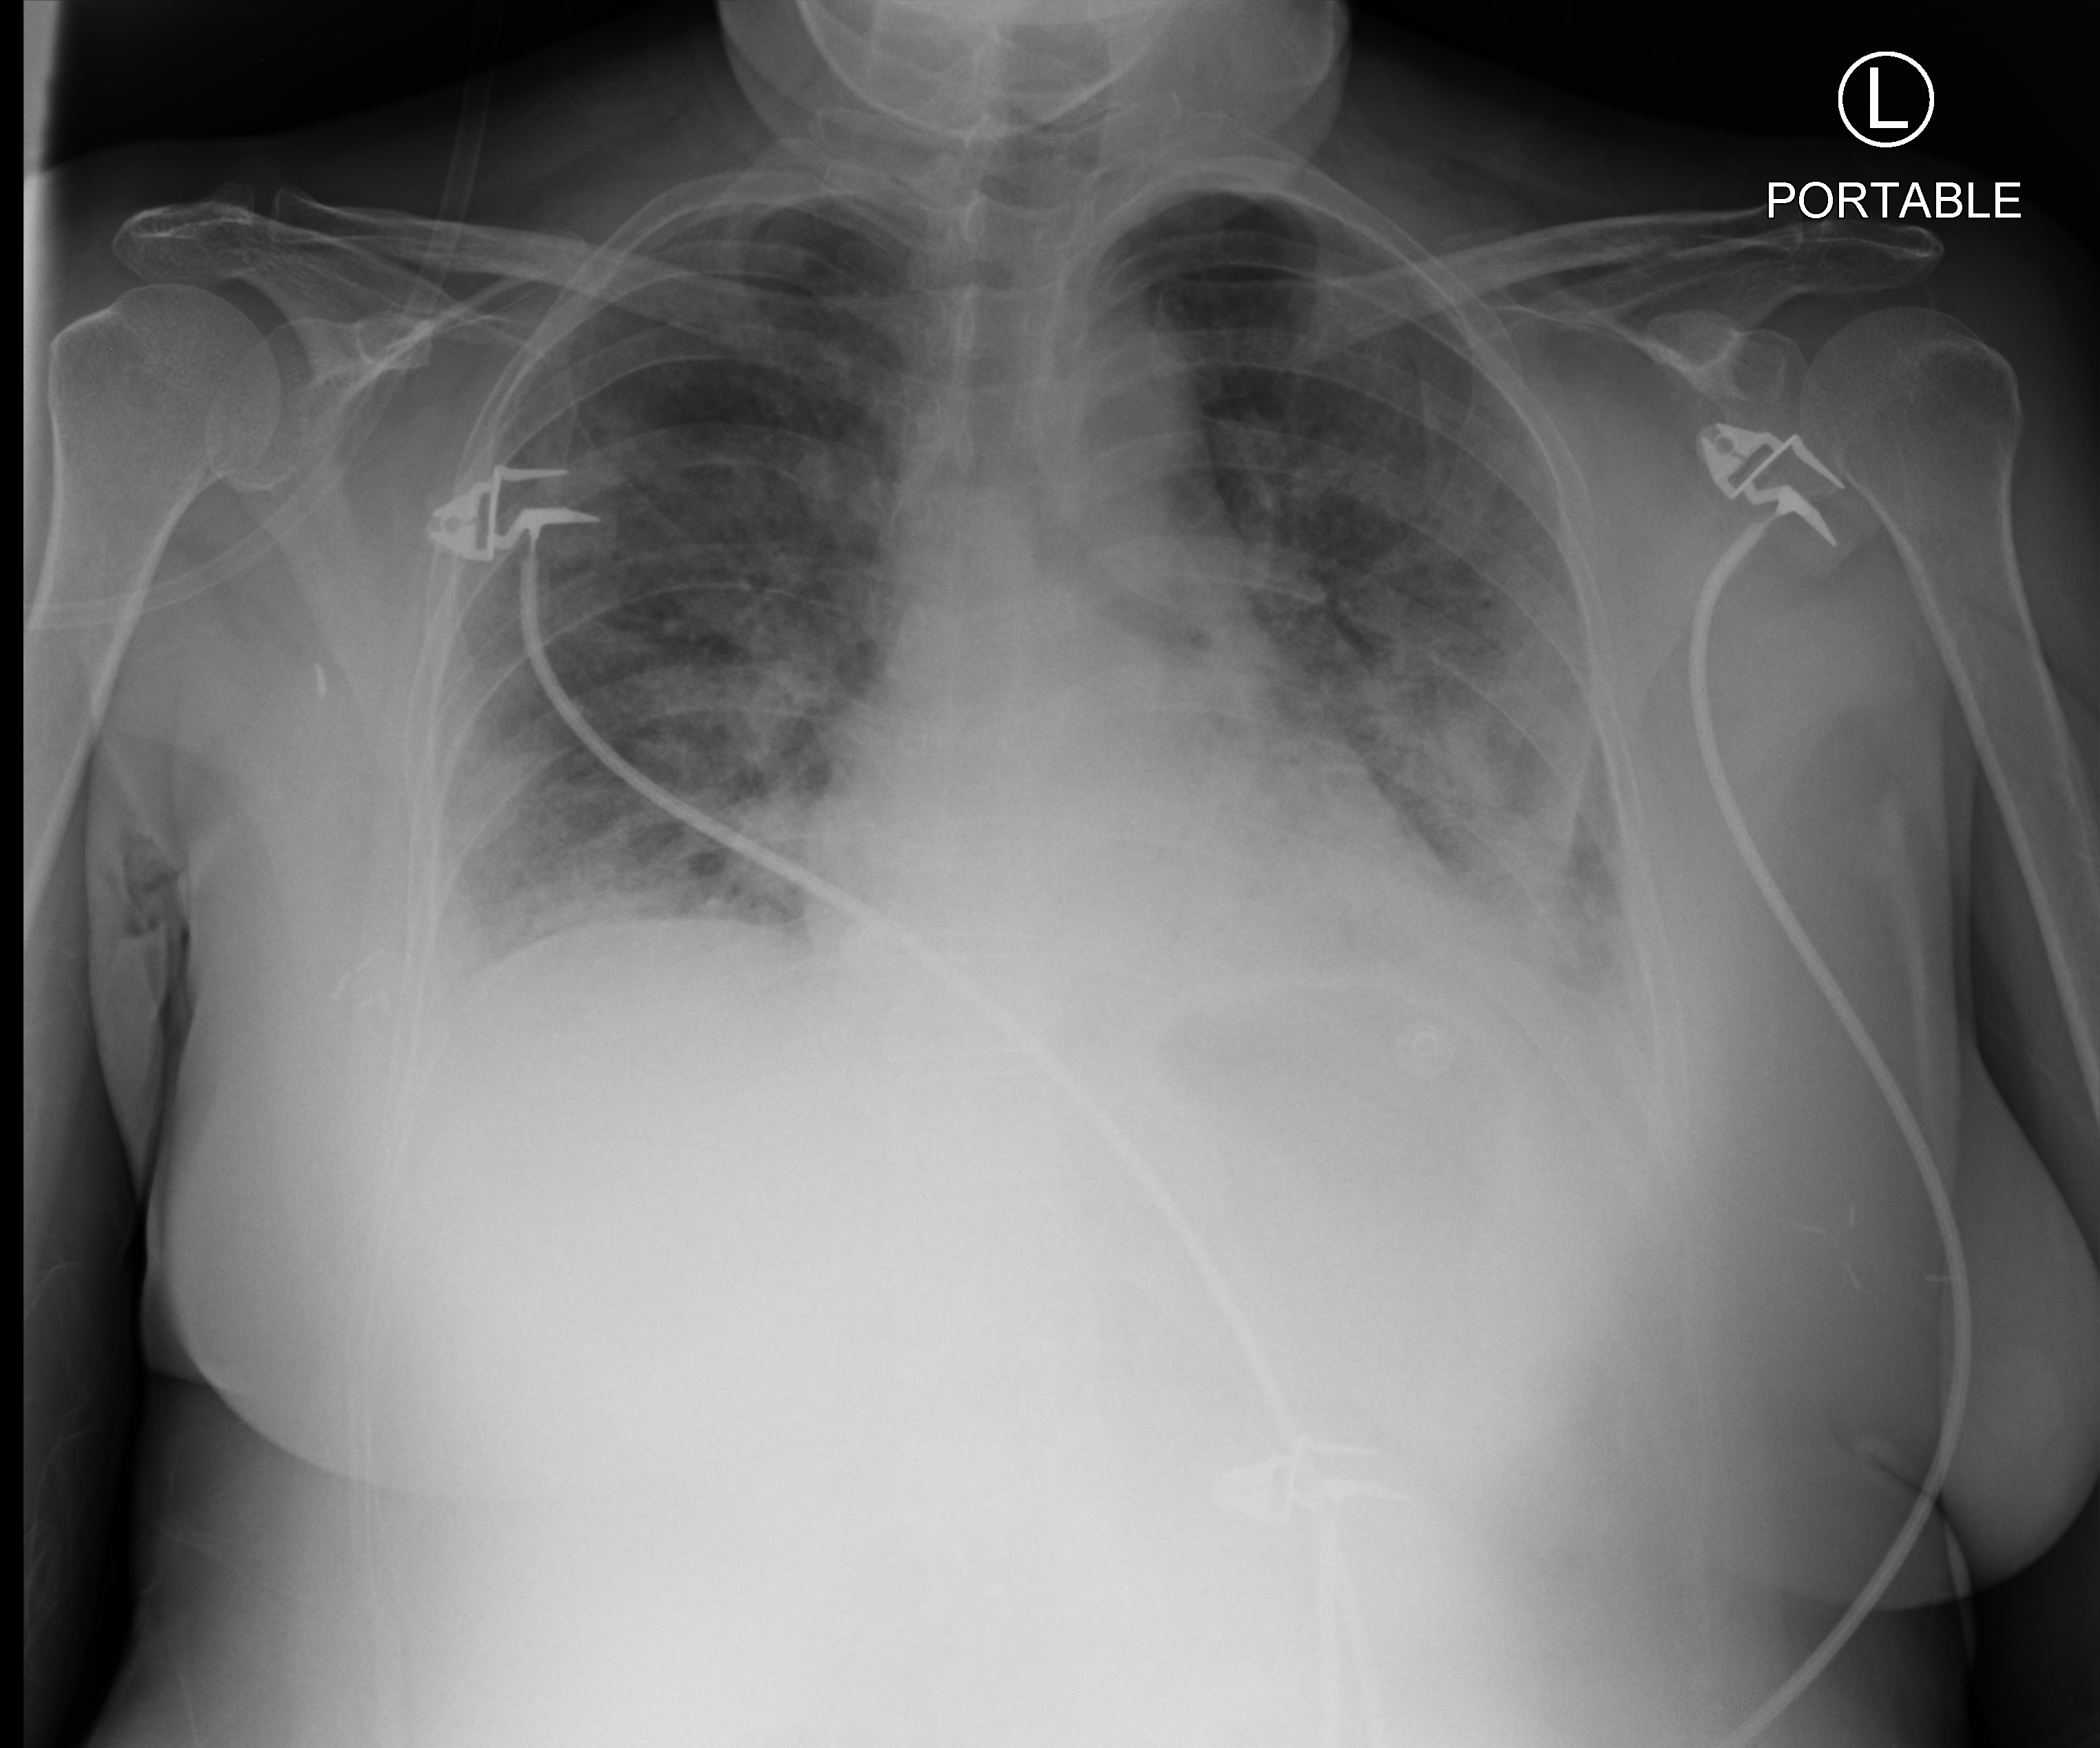
Bedside chest radiograph (computed radiography); anteroposterior (AP) projection. Patient hospitalised with COVID-19; female, aged 18–59 years.
Hospital-stay facts (about this admission, not read from this image; timing relative to this image not recorded): hypertension (admission record): no; smoking status (admission record): never.